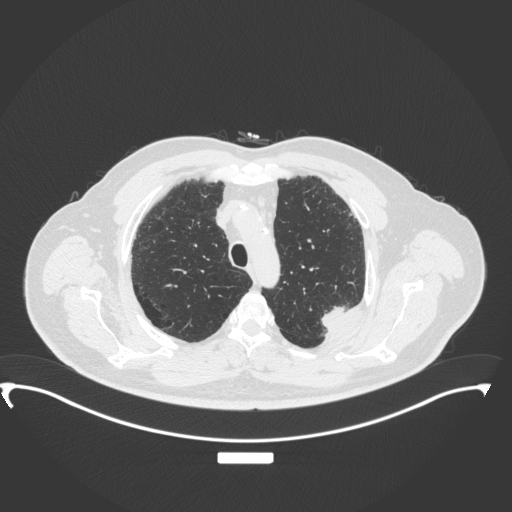
Chest CT, one axial slice. Position 283 of 350 along the scan axis. Reconstruction kernel B31f. Lung window (W 1500 / L -600 HU). 1 mm slice thickness. 512 × 512 image matrix. Patient: male, 64 years. From the clinical record (not read from this slice): clinical TNM (as recorded): T1c N1 M1.
Structures marked on this image (rectangle marked by the reading radiologist):
- lung tumour (recorded histology: adenocarcinoma): bounding box (x1, y1, x2, y2) in pixels: (318, 299, 351, 337)